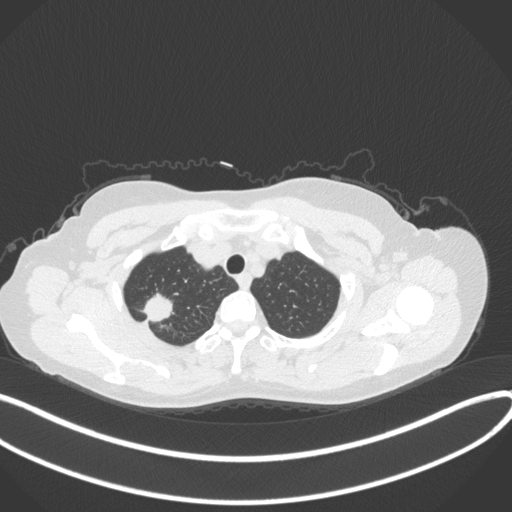
Chest CT, one axial slice. Lung window (W 1500 / L -600 HU). 512 × 512 image matrix, field of view 400 × 400 mm. Female patient, age 50 years. Case-level facts recorded for this patient, not image findings: clinical TNM (as recorded): T1c N0 M0; histopathological grade: G2-3.
Annotated regions visible in this slice (rectangle marked by the reading radiologist):
- lung tumour (recorded histology: adenocarcinoma): box from (x=138, y=293) to (x=175, y=325) px